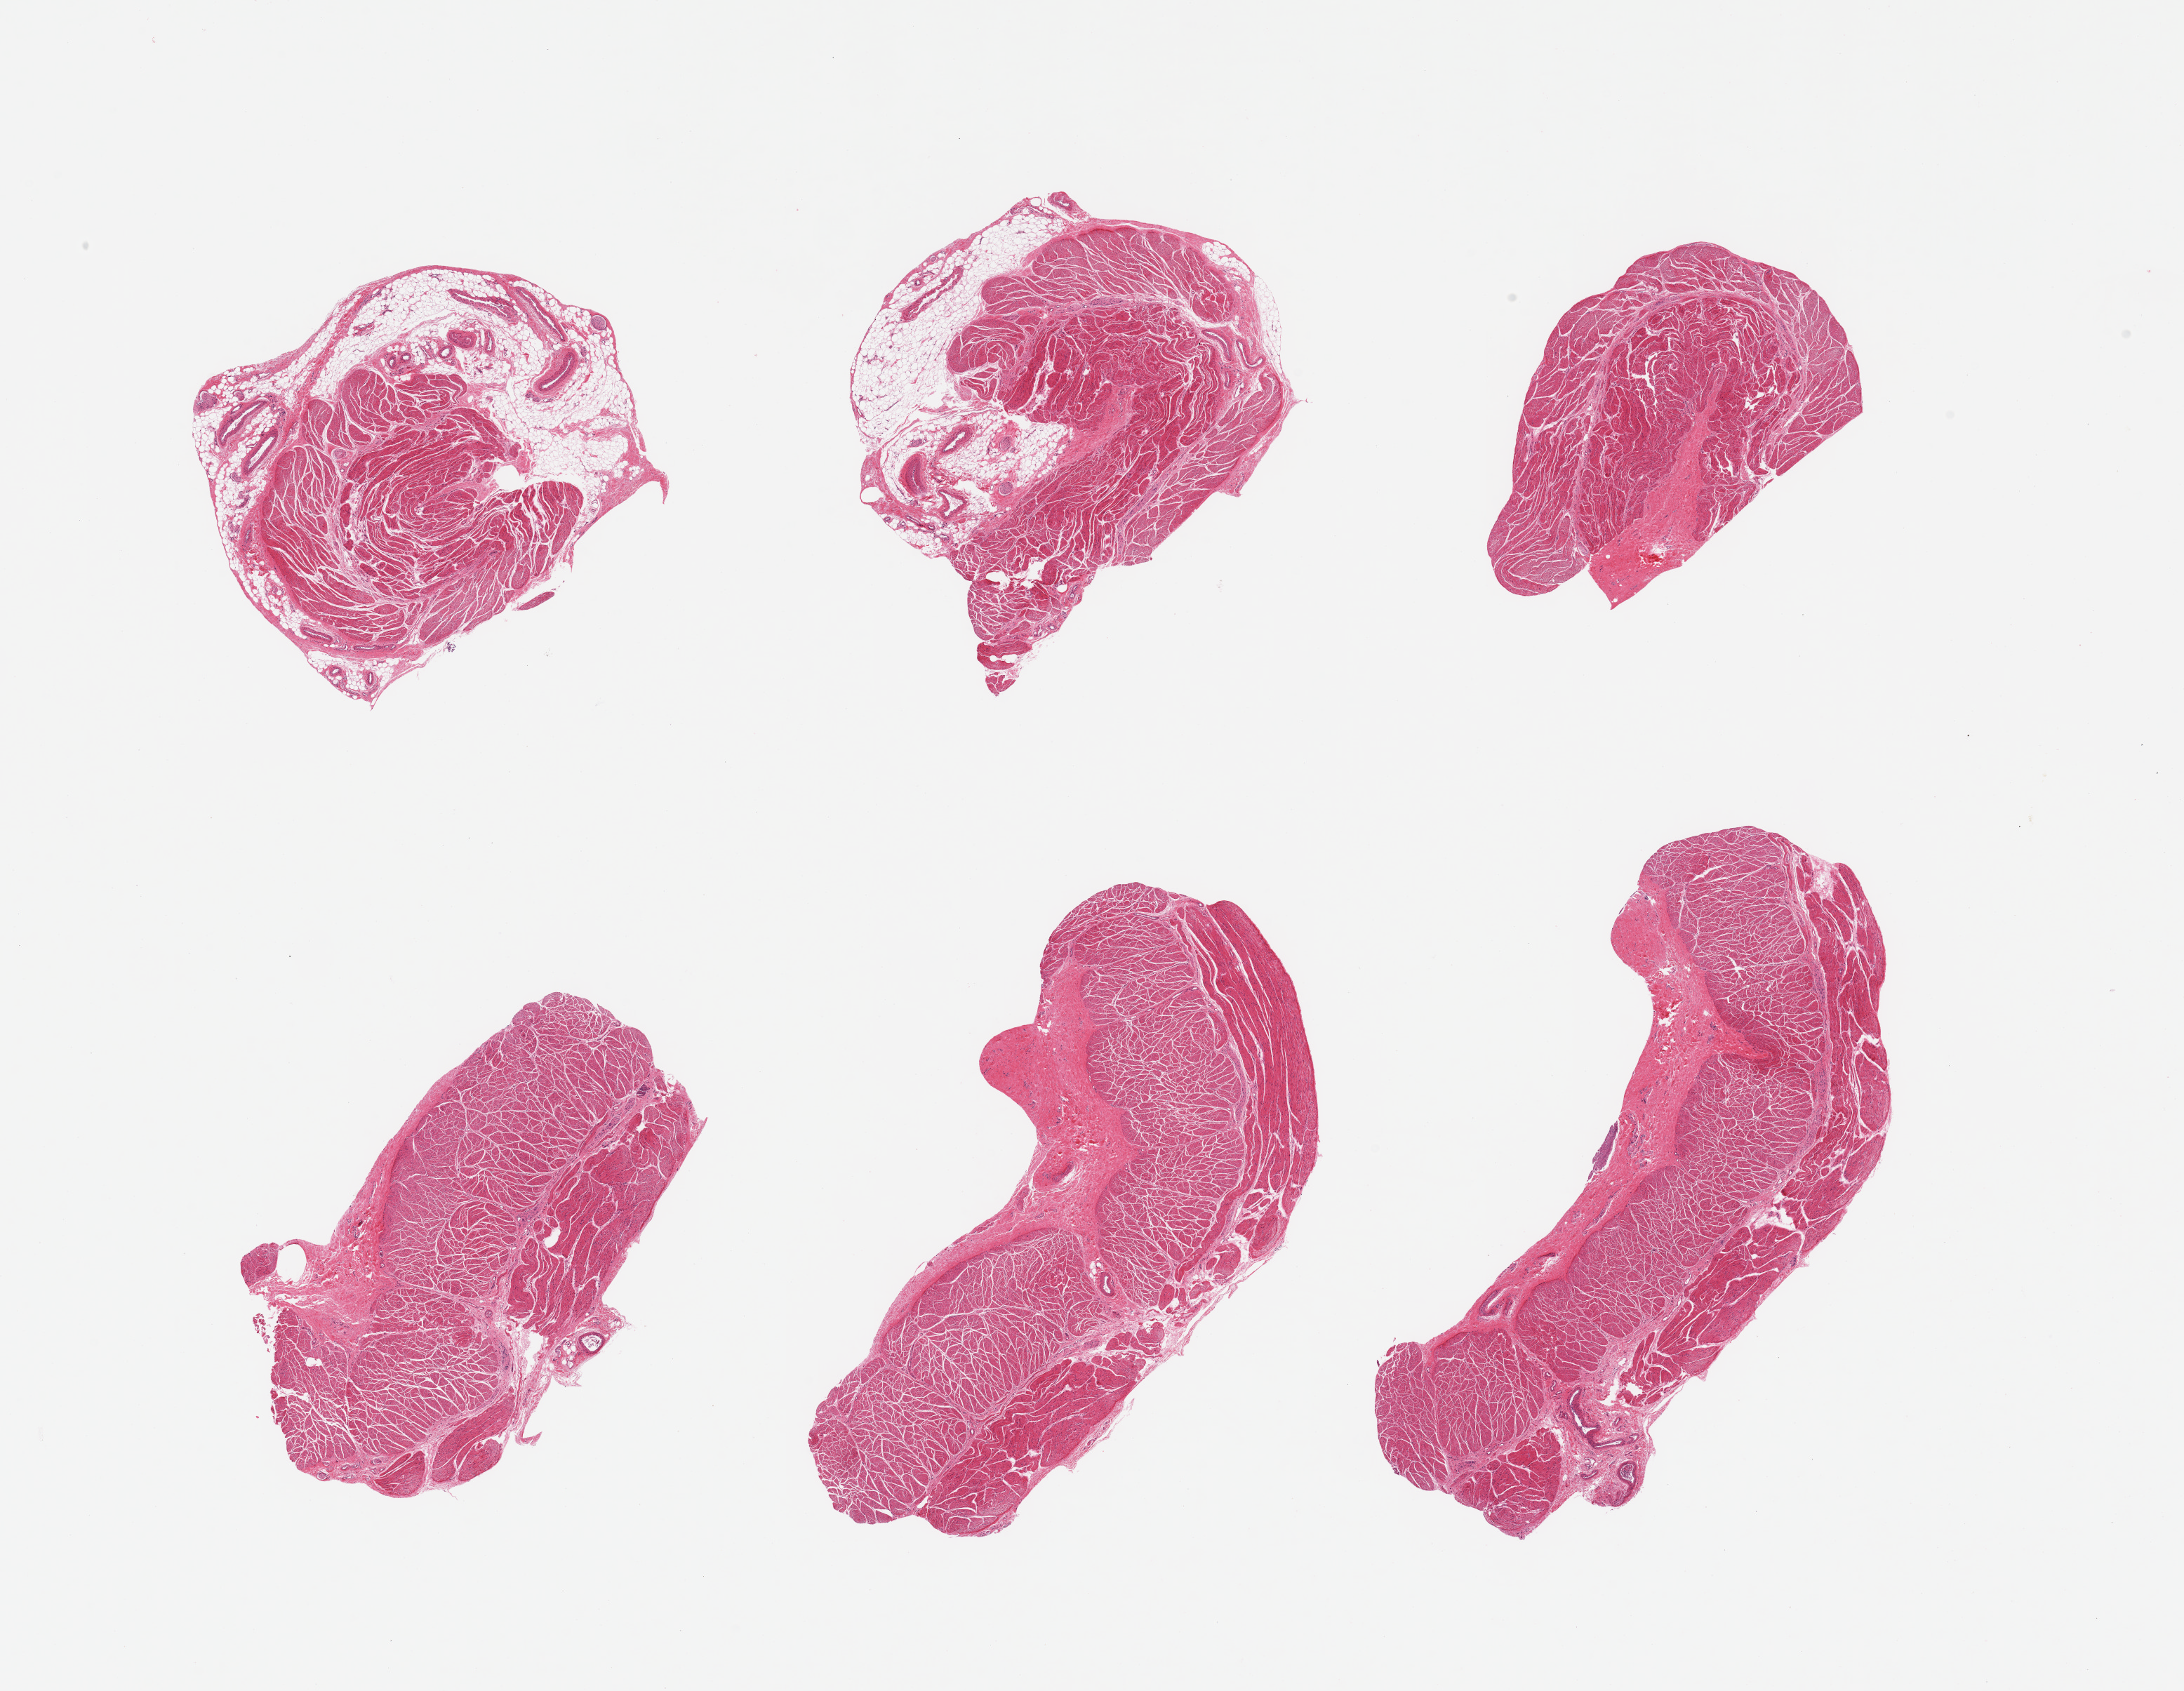
Haematoxylin and eosin whole-slide image, low-resolution overview of the scanned area, about 24.6 x 19.1 mm (acquisition: 20x scan); PAXgene-fixed paraffin-embedded (PFPE) section; sampled site (target tissue): esophageal muscle; tissue donor sample. Donor: male.
- pathologist's review note for this sample: 6 pieces, confirmed target muscularis; few adherent nubbins of serosal fat, ~1-2mm